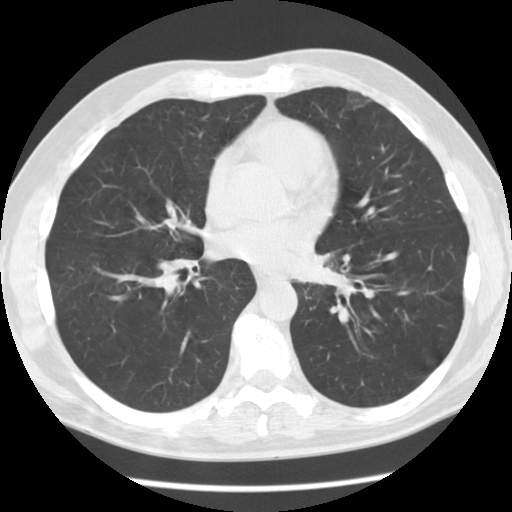
Chest CT (low-dose screening protocol), one axial image; baseline annual screen; lung window (W 1500 / L -600 HU); 2.5 mm slice thickness; 120 kVp. Male participant, aged 55 years at enrolment. Former smoker at enrolment.
• Expert reader's lesion annotation, box from (x=281, y=235) to (x=348, y=303) px.
• No non-calcified nodule or mass ≥4 mm was recorded by the screening reader at this exam.
• Official screen result: negative screen, minor abnormalities not suspicious for lung cancer.
• Later outcome: lung cancer diagnosed 223 days after this screen — squamous cell carcinoma, NOS, left lower lobe, moderately differentiated (G2), stage IV (AJCC 6th edition), 51 mm at pathology.